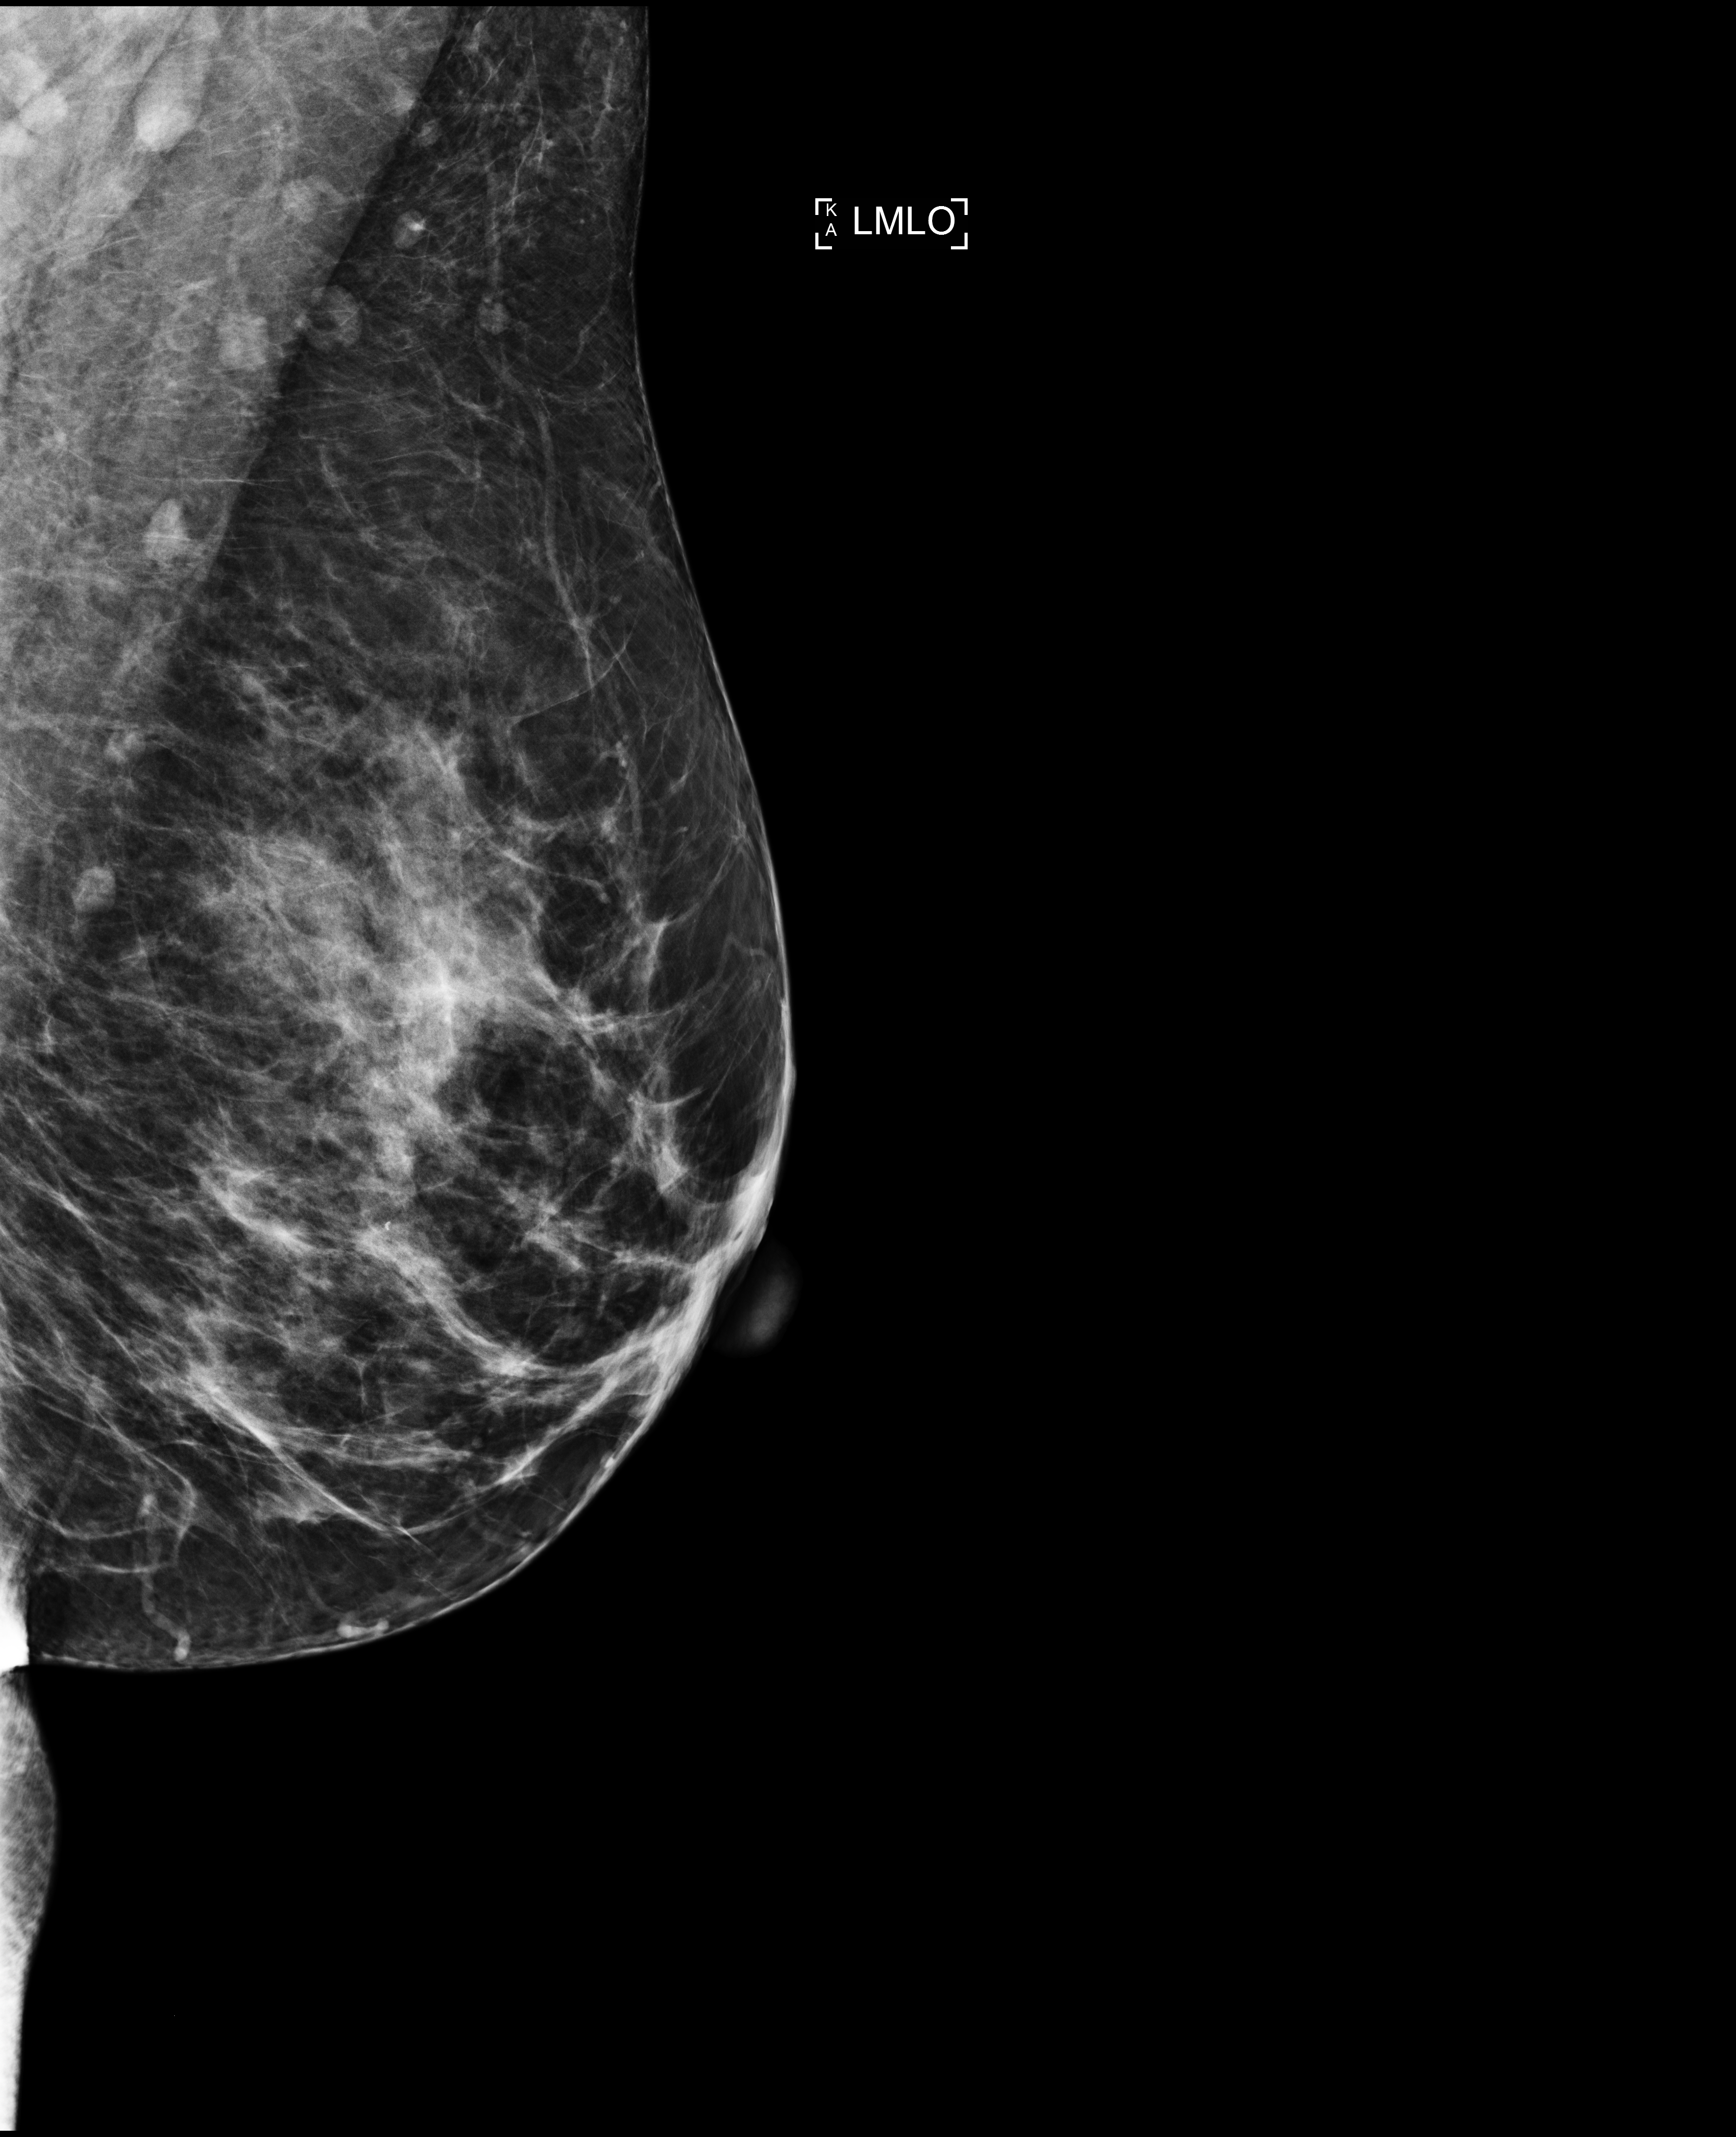
Screening examination. Female patient, age 47 years.
Image type: full-field digital mammogram. Breast: left. Projection: MLO view.